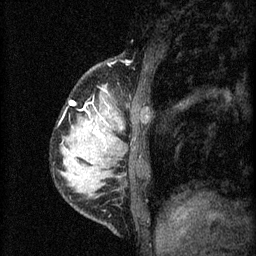
Breast MRI (dynamic contrast-enhanced), one sagittal slice; position 13 of 60 along the scan axis; 3 images stored at this slice position (order not interpretable as contrast timing); 1.5 T; TE 4.2 ms, TR 8.2 ms; 2 mm slice thickness; 256 × 256 image matrix, field of view 180 × 180 mm. Female patient, age 37 years.
Outlined on this slice (semi-automatically segmented with operator editing):
- analysis volume of interest (the breast-tissue region the enhancement analysis was run in; not a lesion): bounding box [x1, y1, x2, y2] px = [58, 84, 140, 181]
- tumour enhancement mask (voxels above the 70 % enhancement threshold inside the analysis volume of interest): [69, 90, 108, 141]